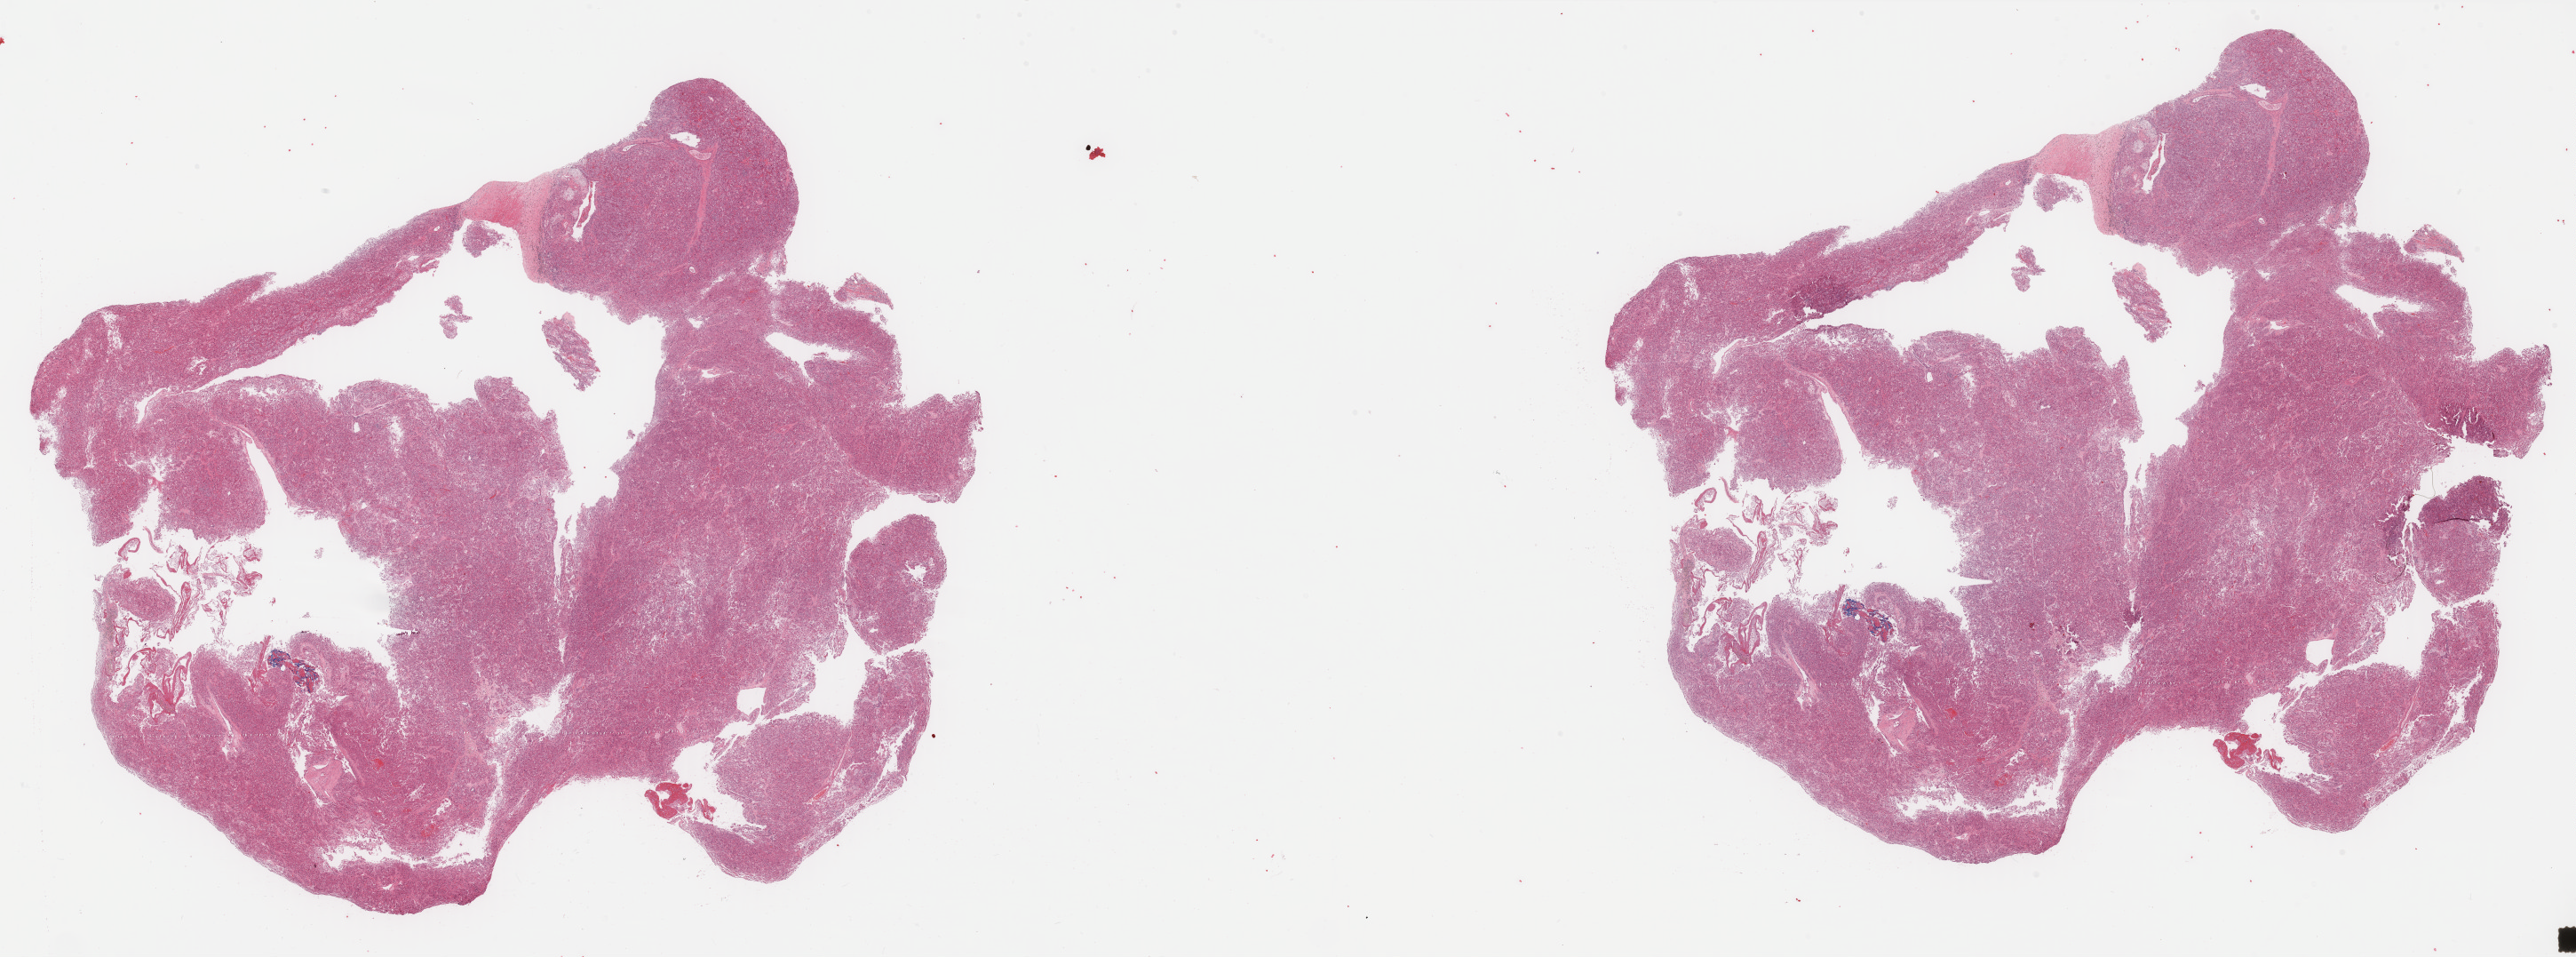
Digitized H&E-stained tissue section (whole slide), whole scanned area (about 45.9 x 17.0 mm, acquisition: 40x scan) shown as a low-resolution overview, FFPE section, sample: primary tumour, kidney. Female patient; age at initial diagnosis 62 years. Histologic grade: G3 (poorly differentiated).
Diagnosis: Renal cell carcinoma, NOS. Laterality: right. AJCC pathologic stage: I.